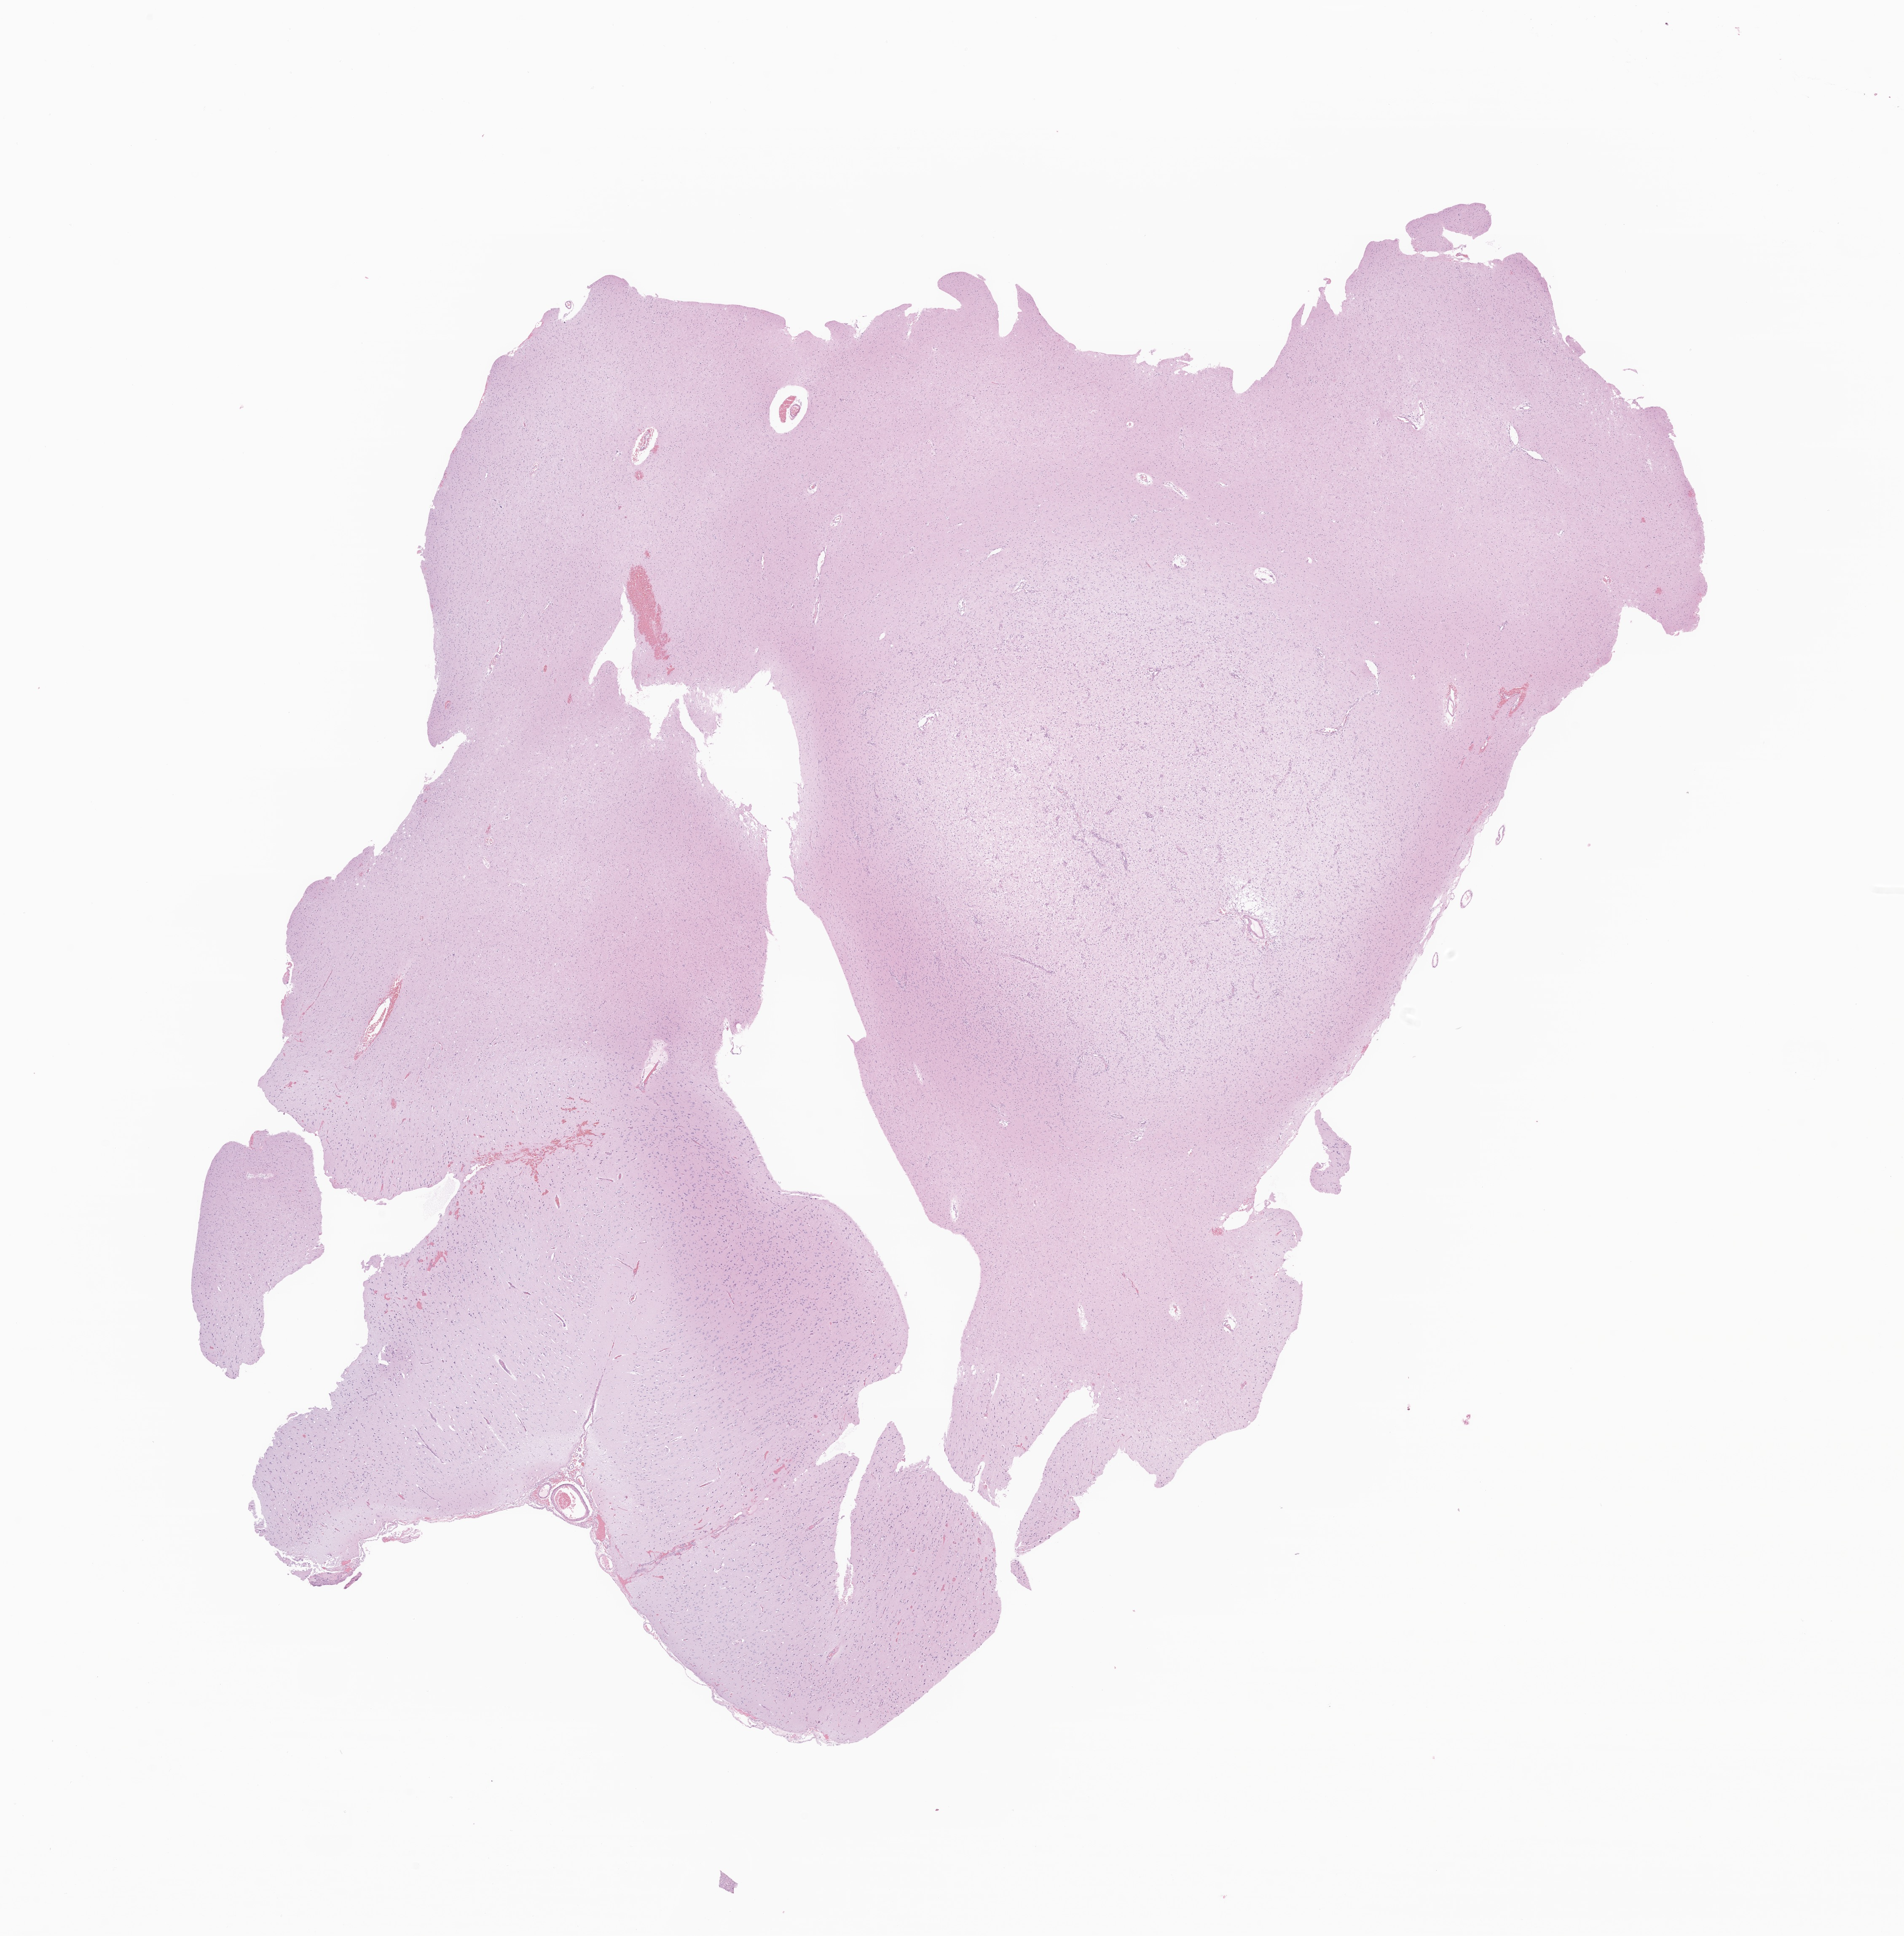
Digitized hematoxylin and eosin (H&E)-stained section of tumor tissue from the brain — a low-resolution overview of the entire scanned area, about 19.0 x 19.4 mm, FFPE section. Patient female; age 81 months (6 years 9 months).
- diagnosis (ICD-O-3 morphology term): Neoplasm, uncertain whether benign or malignant